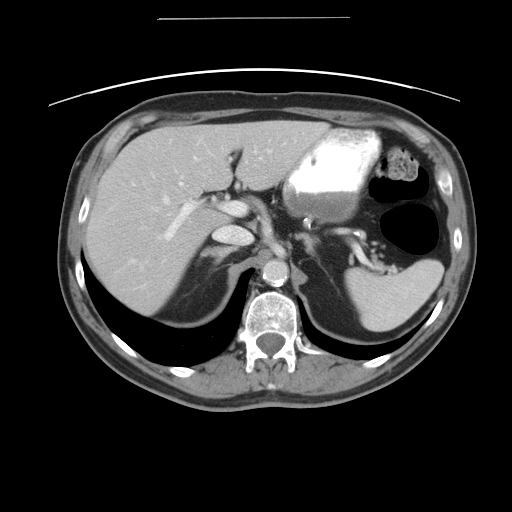
Contrast-enhanced abdominal CT, one axial slice; slice 30 of 49 in the series (ordered by position); reconstruction kernel STANDARD; intravenous contrast given; soft-tissue window (W 400 / L 40 HU); 512 × 512 image matrix. Male patient, age 57 years. From the clinical record (not read from this slice): diagnosis: colorectal cancer liver metastases, imaged before liver resection; multiple liver metastases: yes; largest metastasis: 4 cm; chemotherapy before resection: no.
Annotated regions visible in this slice (outlined manually by an expert reader):
- hepatic veins: bounding box <129,149,270,267> (left, top, right, bottom; pixels)
- liver: <84,120,328,315>
- planned liver remnant (the part of the liver to remain after resection): <209,120,328,223>
- portal vein (with intrahepatic branches): <132,176,245,239>